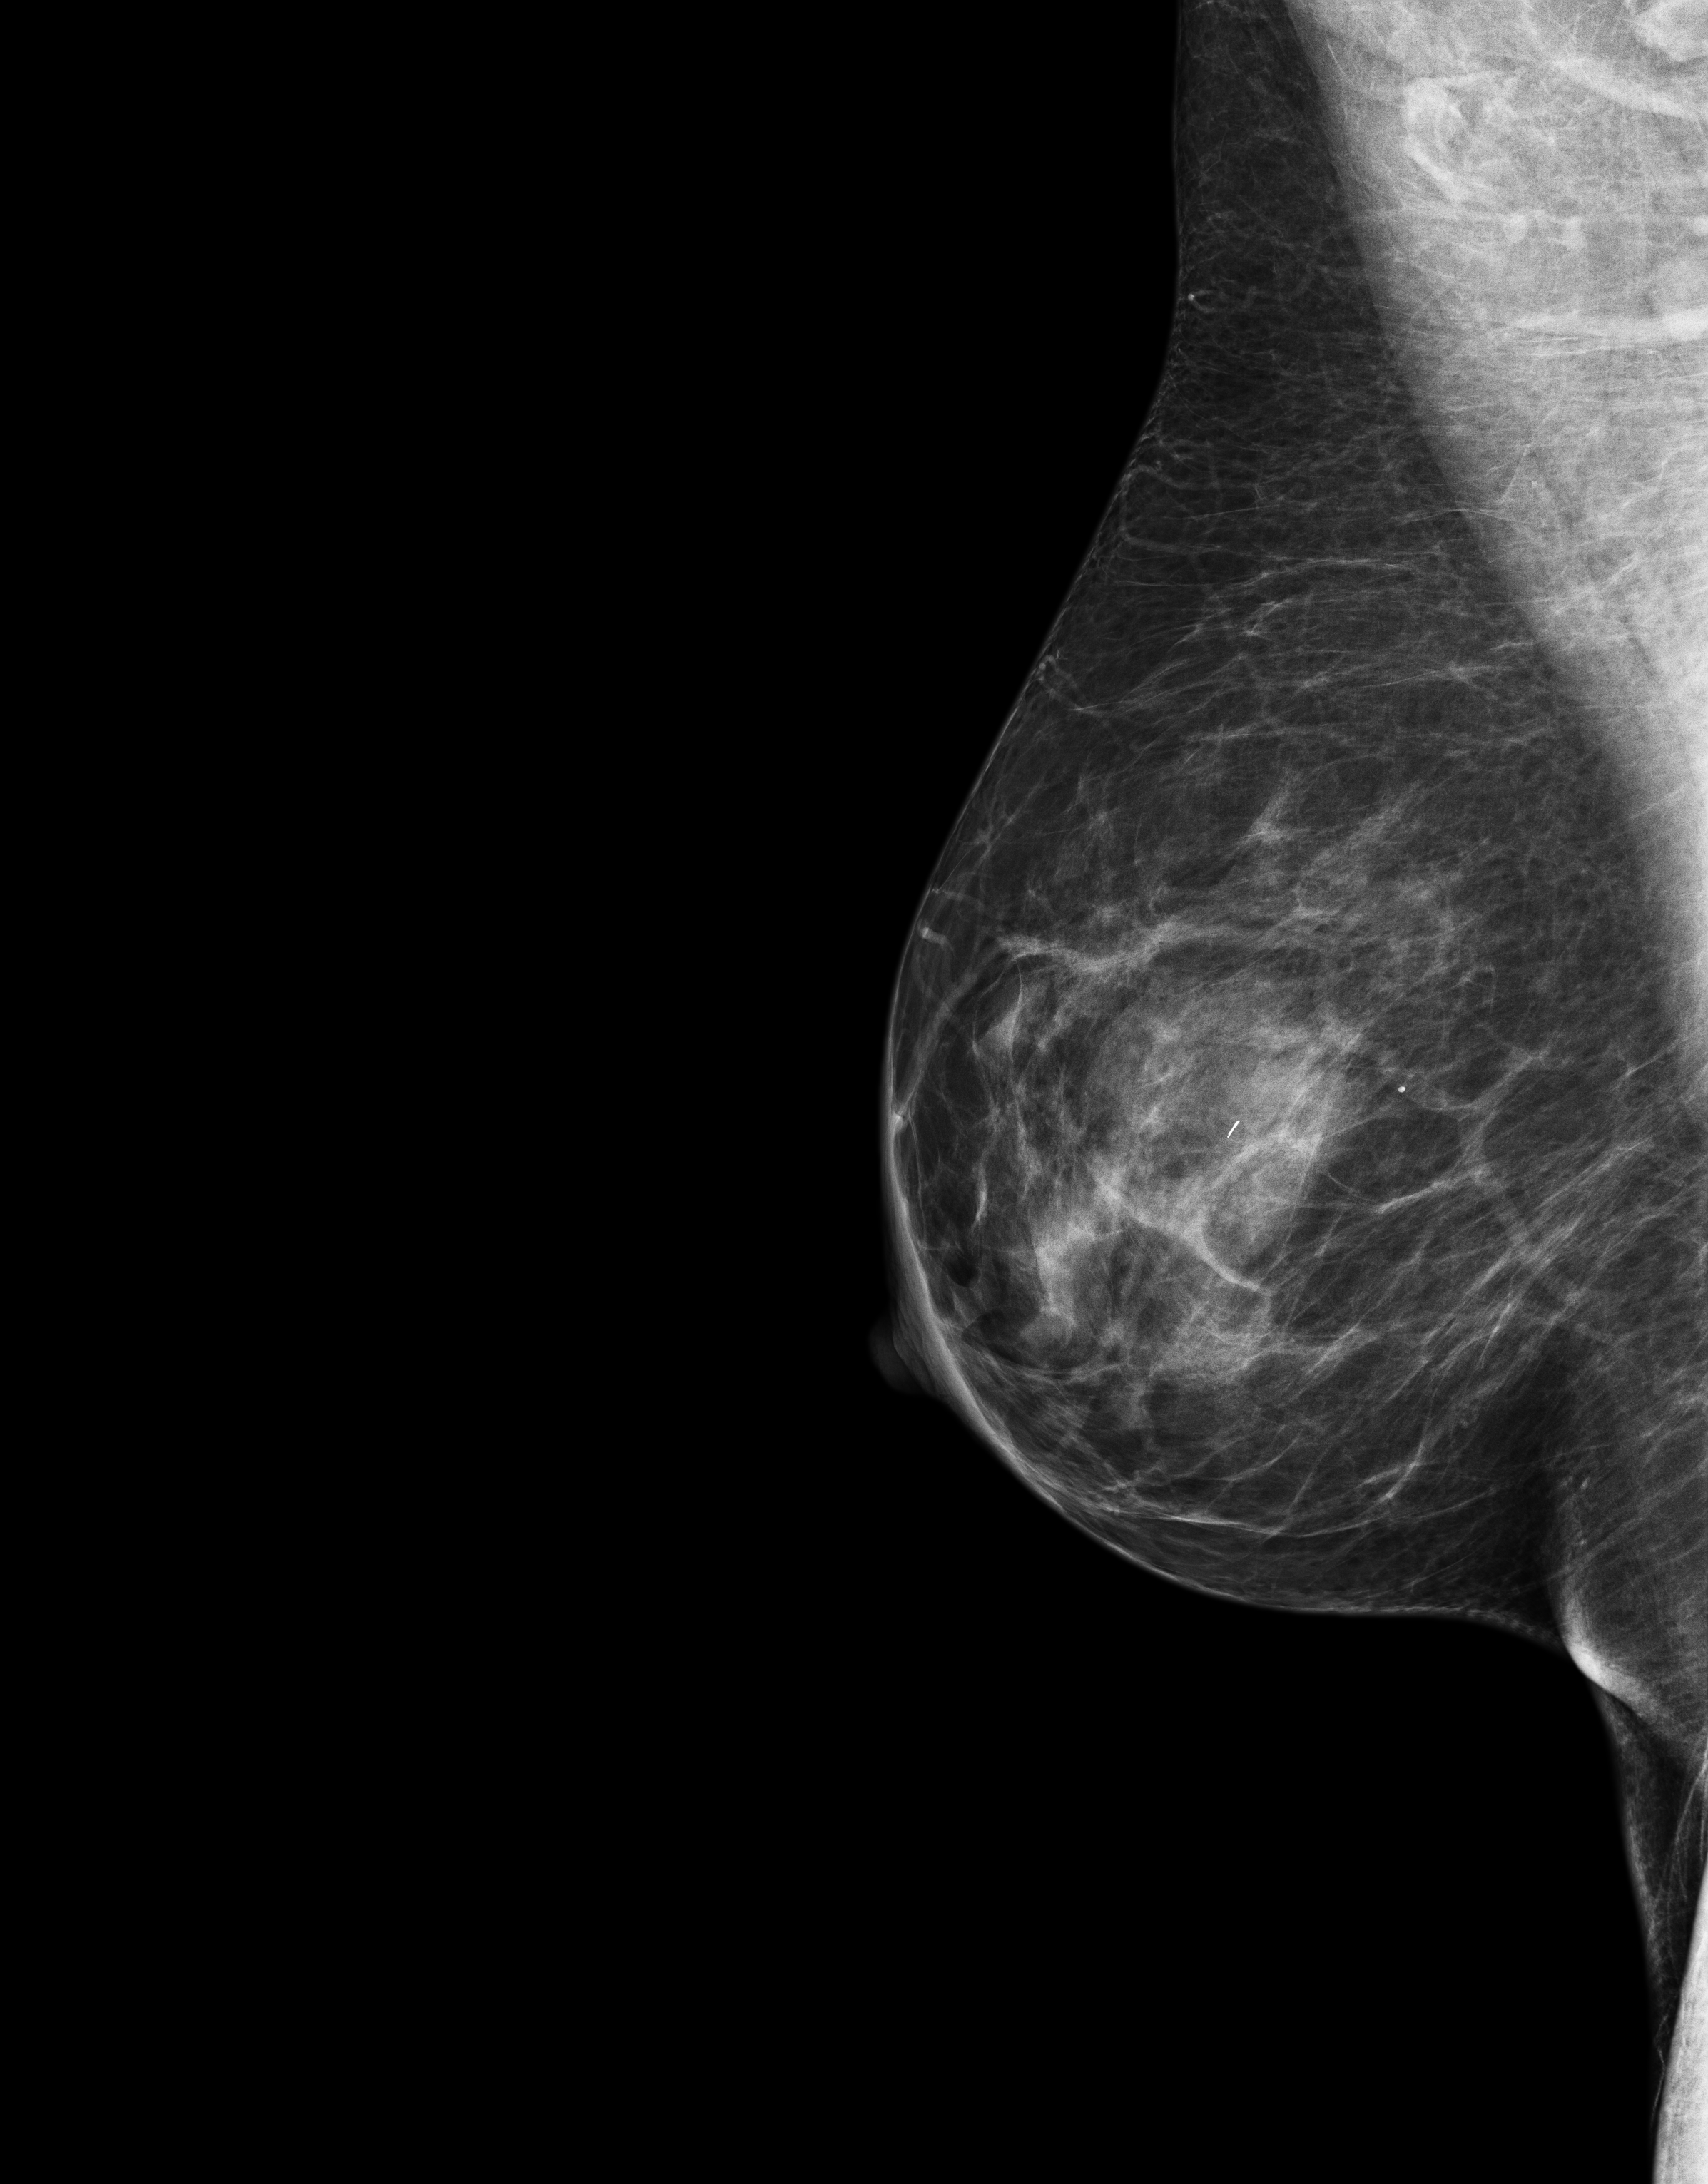
Screening examination; system: Senographe Essential ADS_56.21.3. Patient: female, 48 years.
Image type: full-field digital mammogram. Breast: right. Projection: medio-lateral oblique projection.